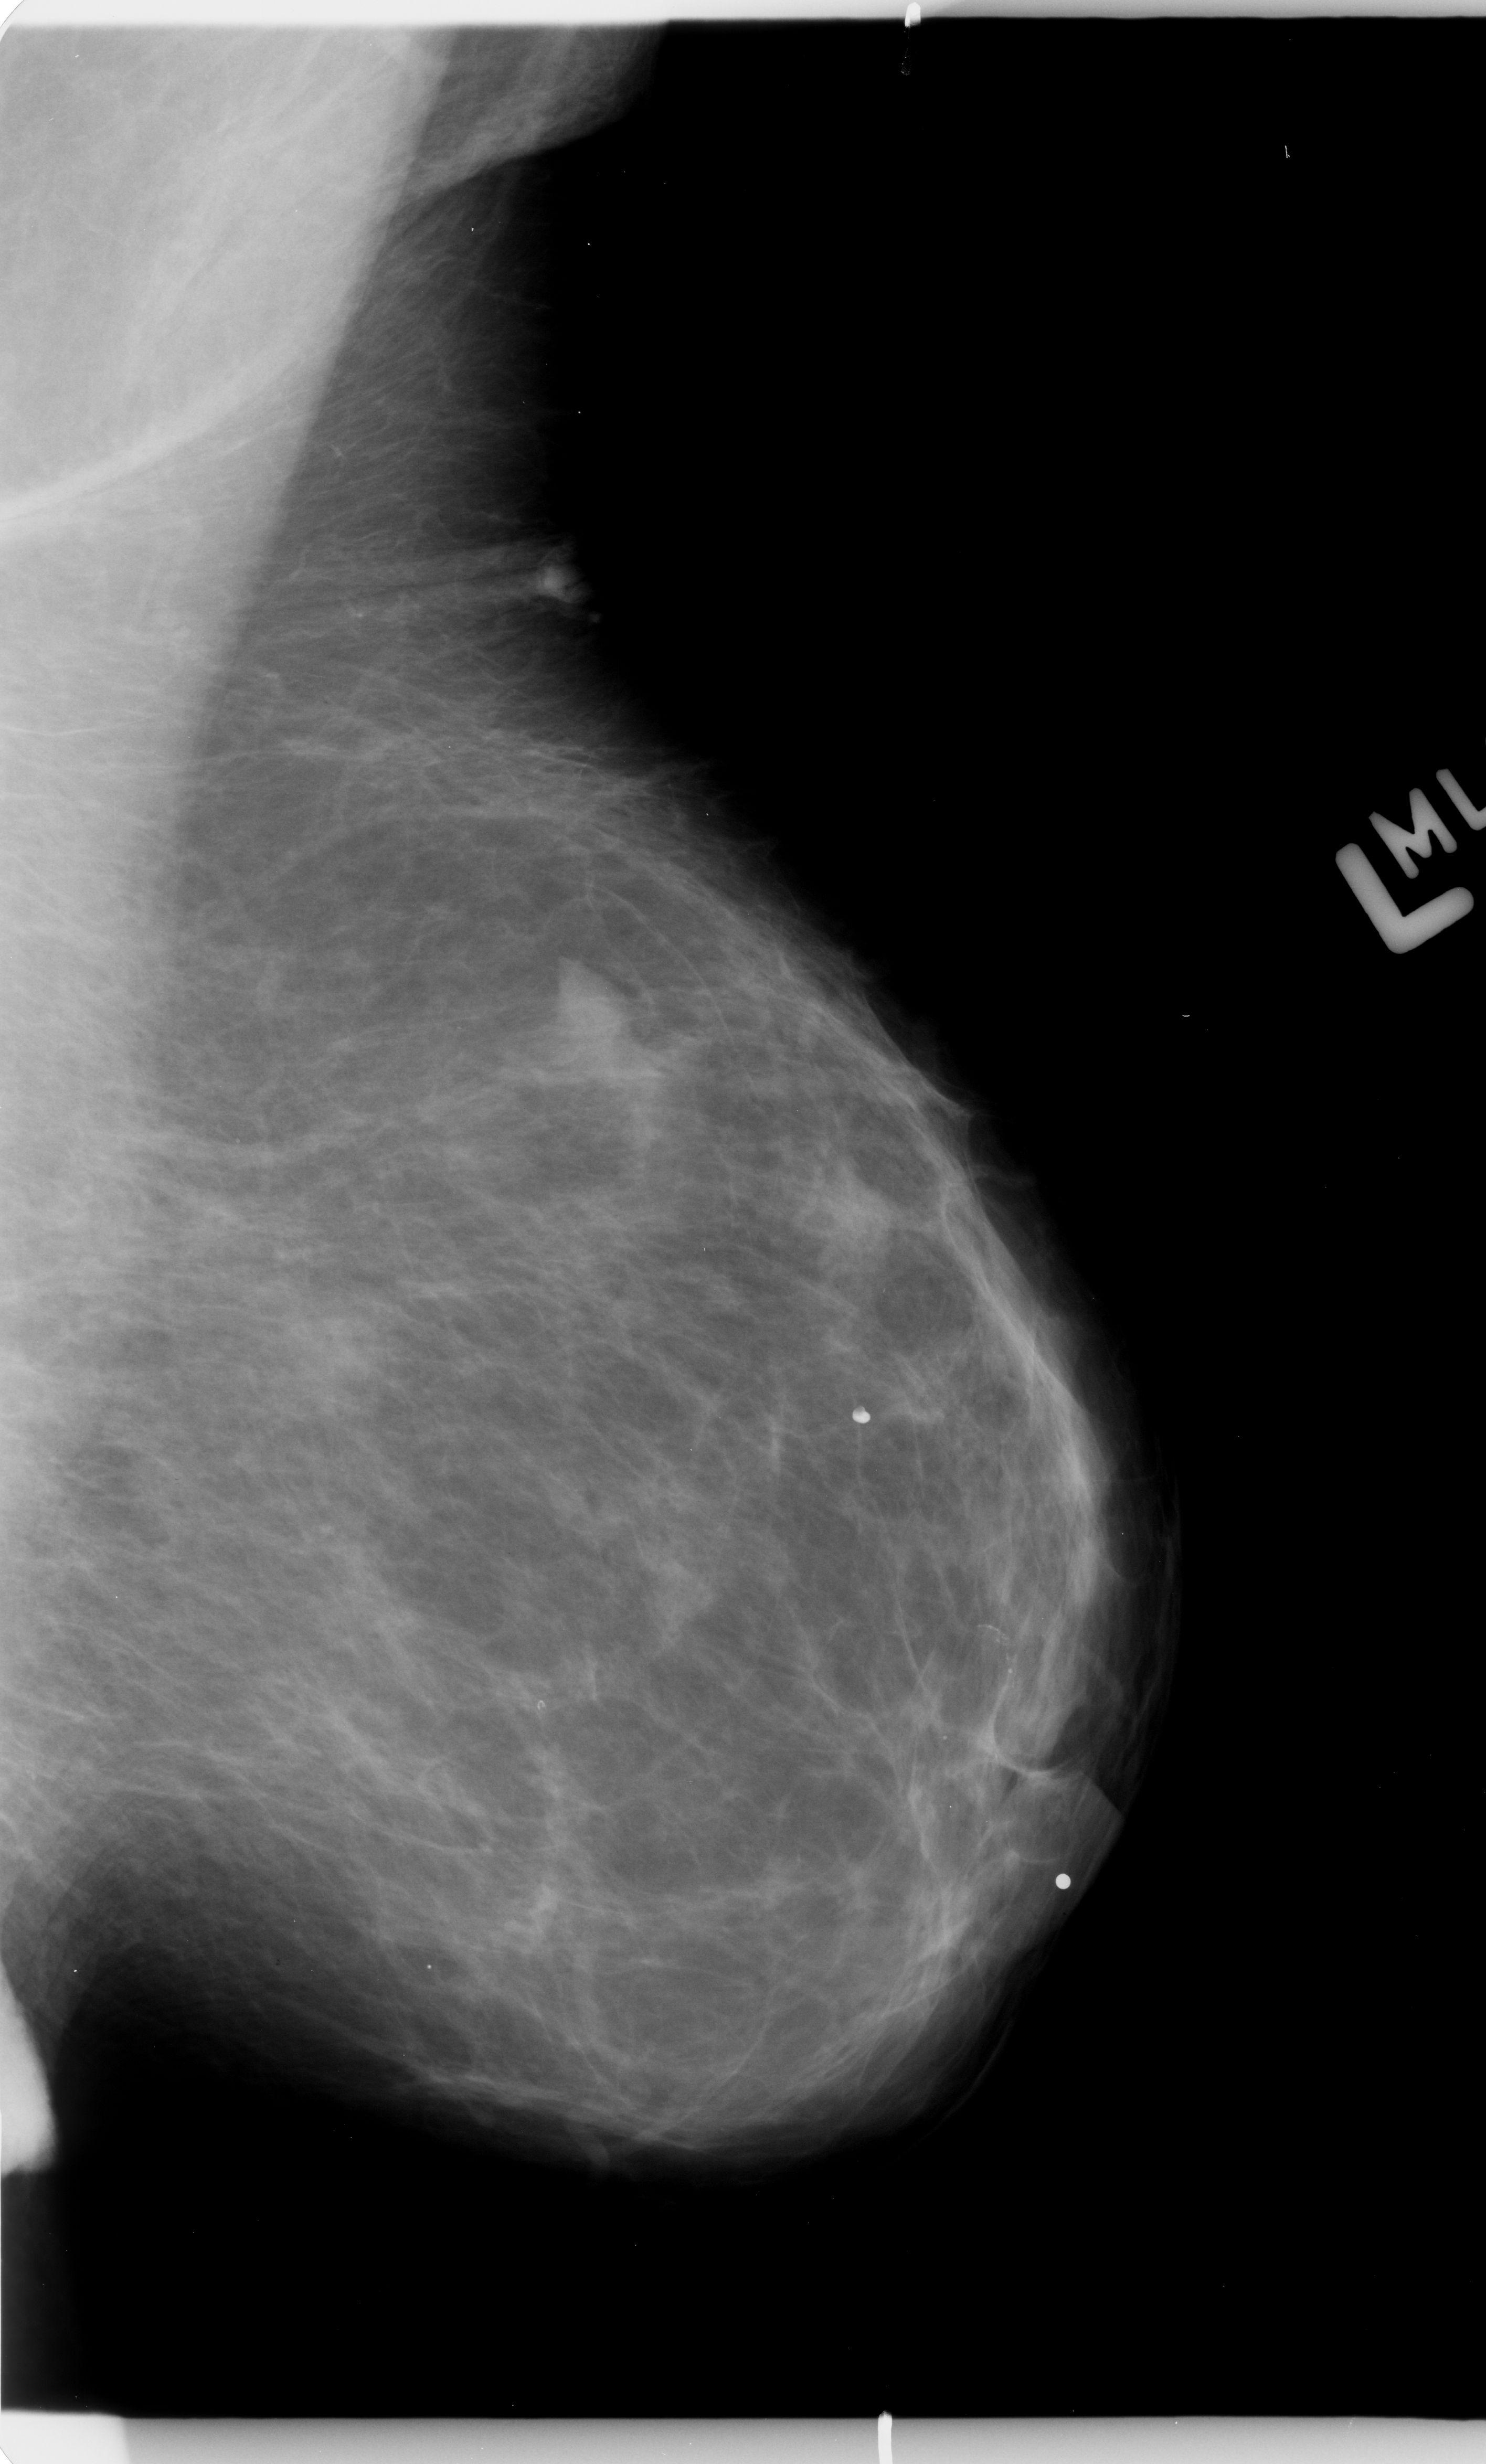
Digitized screen-film mammogram; left breast; mediolateral oblique (MLO) view; BI-RADS breast density category 2 (scale 1–4).
- Mass, shape irregular, margins ill defined; BI-RADS assessment category 4; pathology (as recorded): benign.